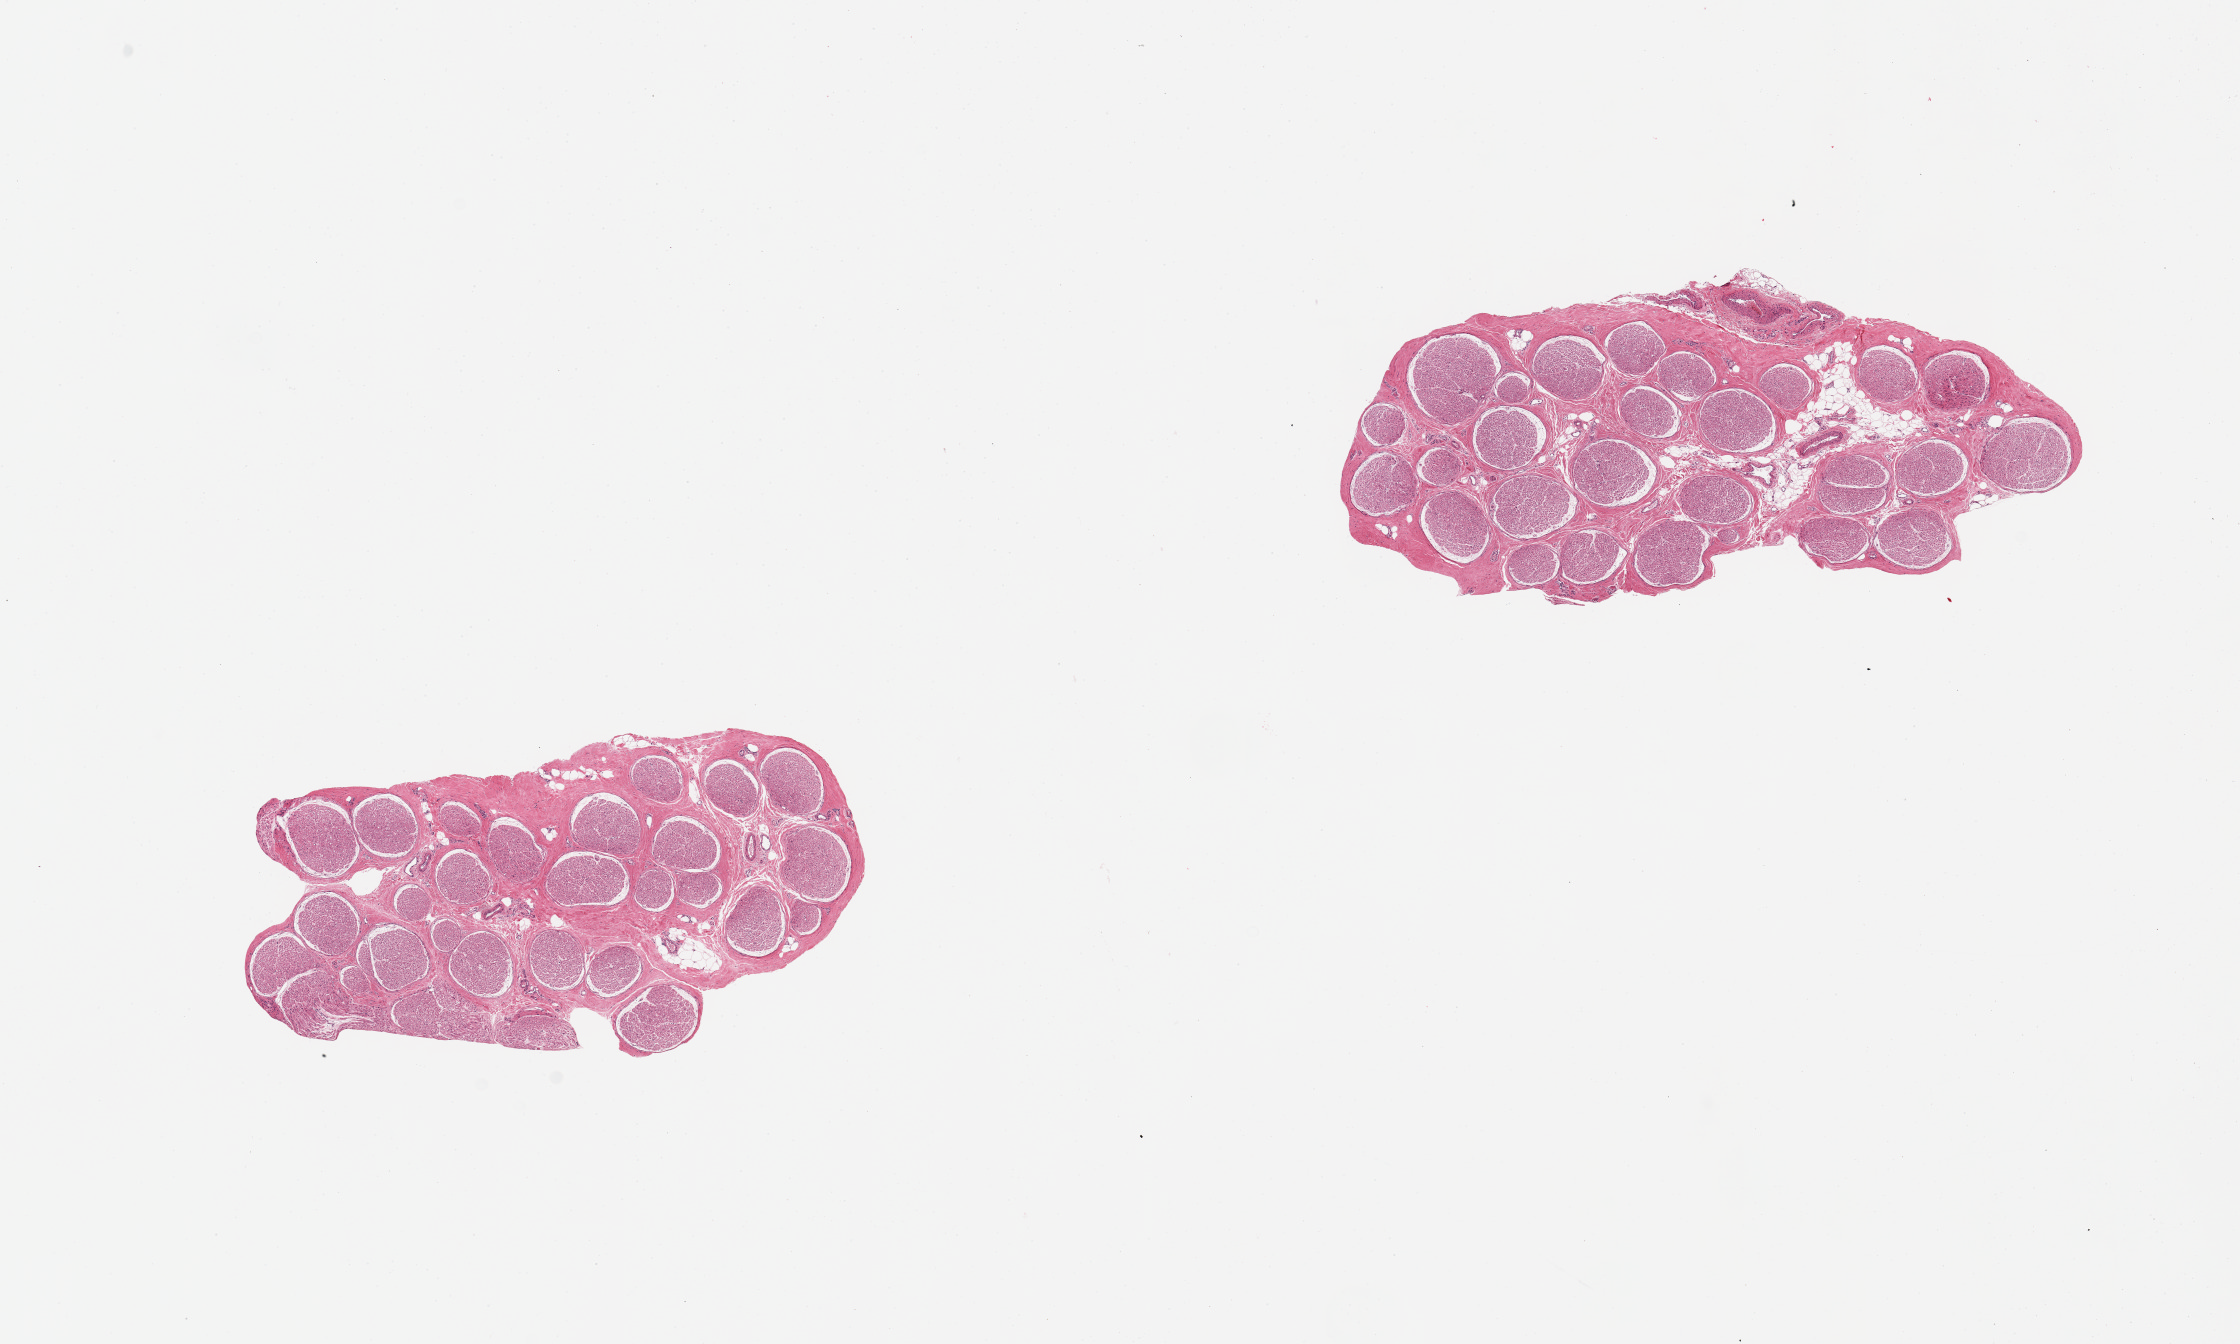
Whole-slide image, H&E stain, a low-resolution overview of the entire scanned area, about 17.7 x 10.6 mm; PAXgene-fixed paraffin-embedded (PFPE) section; section of tibial nerve (target tissue); donor tissue sample. Donor sex: male.
• pathologist's review note for this sample: 2 pieces; well trimmed; 5 & 10% internal fat